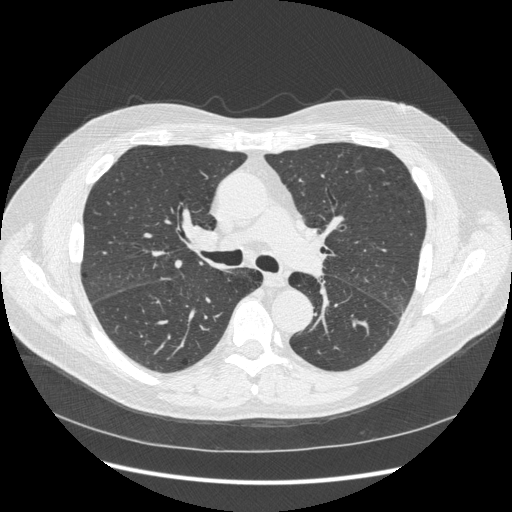
Chest CT (low-dose screening protocol), one axial image, second screening round (one year after baseline), lung window (W 1500 / L -600 HU), 1.25 mm slice thickness, standard (soft-tissue) reconstruction kernel (STANDARD), 120 kVp, slice 109 of 266 in the series, 512 × 512 image matrix, field of view 389 × 389 mm. Male participant, aged 59 years at enrolment.
Expert reader's lesion annotation, bounding box [x1, y1, x2, y2] px = [172, 214, 235, 260]. Reader record for this screening exam (exam-level; its link to the box is not recorded): non-calcified nodule or mass ≥4 mm, lingula, 5 × 5 mm, smooth margins, soft tissue attenuation, pre-existing on the prior screen: yes; interval growth: no. Note: the box lies in the patient's right hemithorax on this image, whereas the reader's record names the left lung; they may be different findings. Official screen result: positive, change unspecified: nodule(s) >= 4 mm or enlarging nodule(s), mass(es), or other non-specific abnormalities suspicious for lung cancer. Participant outcome: lung cancer diagnosed 540 days after this screen — squamous cell carcinoma, keratinizing, NOS, right hilum, stage IIIB (AJCC 6th edition).